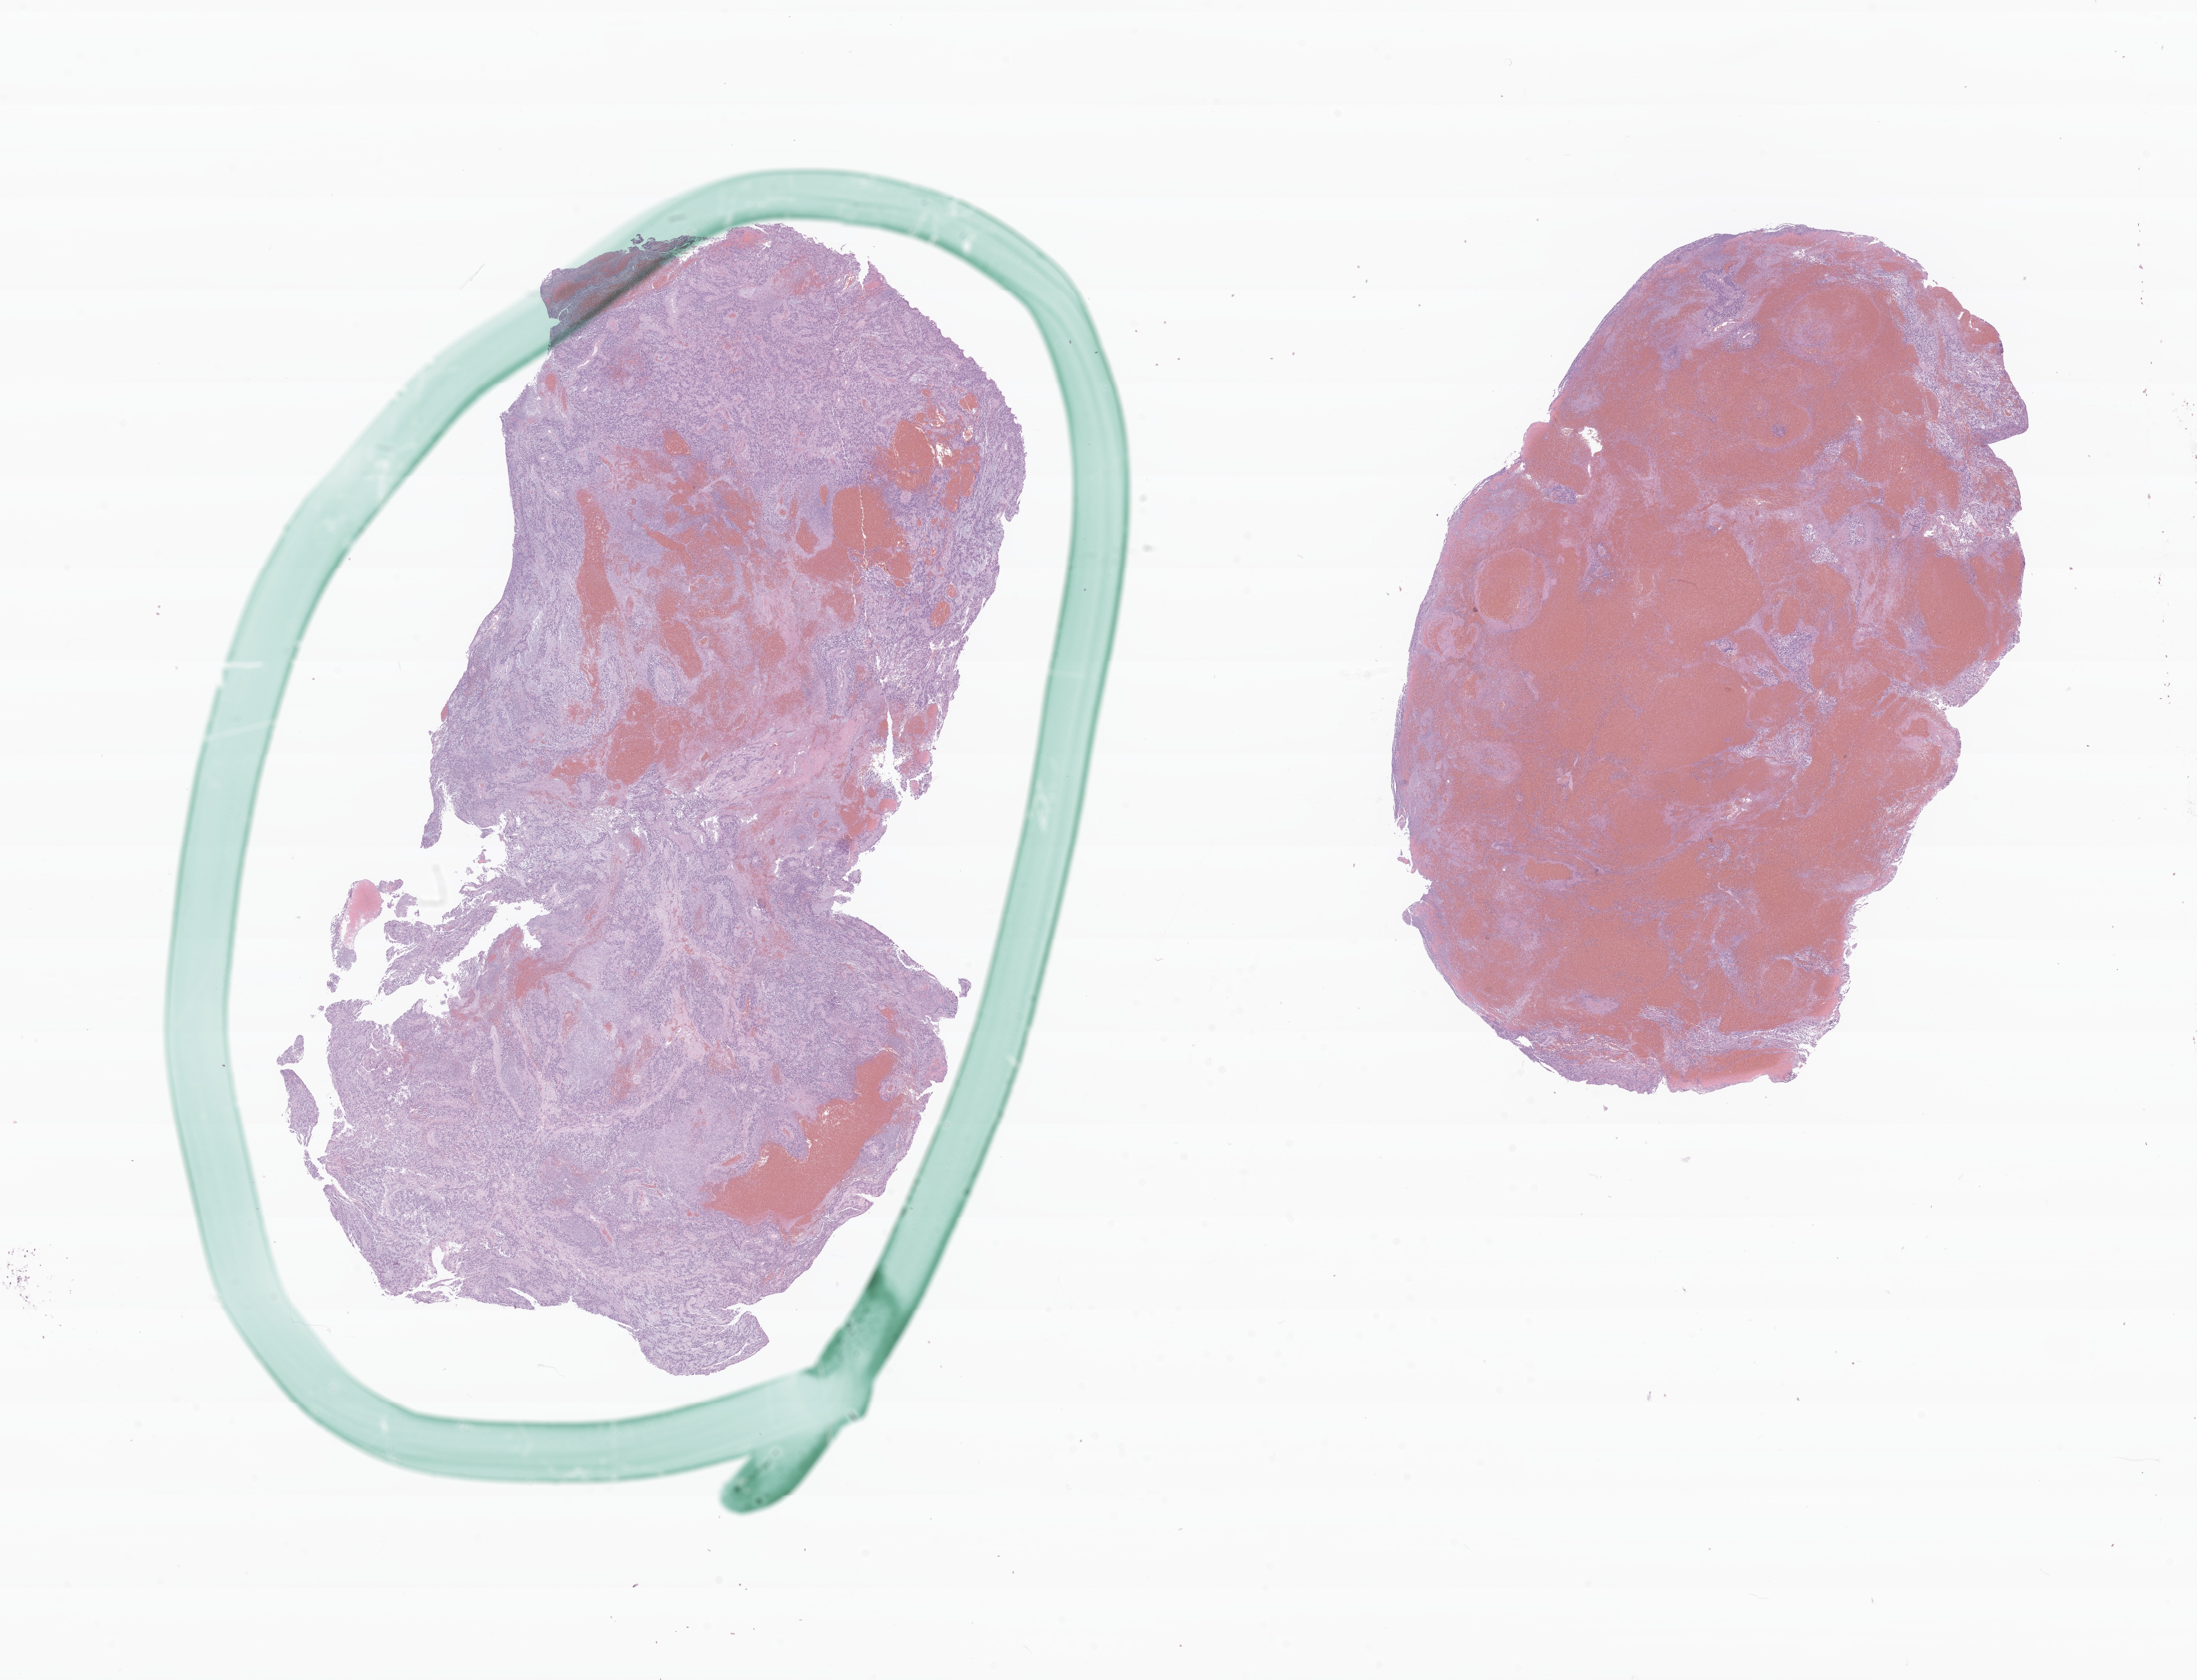
Digitized hematoxylin and eosin (H&E)-stained section of tumor tissue from the spinal cord — low-resolution overview of the scanned area, about 25.2 x 19.3 mm; formalin-fixed paraffin-embedded section. Female patient, age 183 months (15 years 3 months).
Recorded diagnosis: Myxopapillary ependymoma.